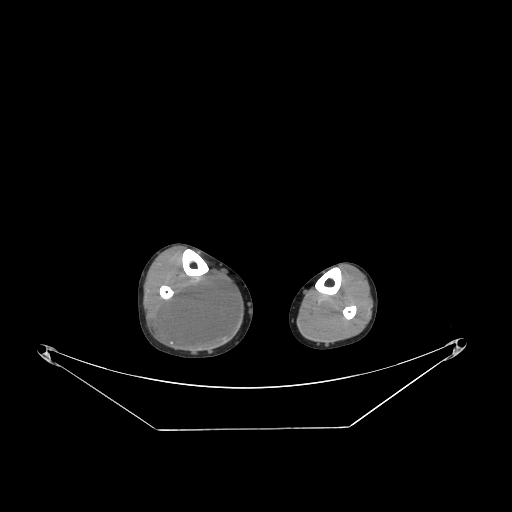
CT of an extremity soft-tissue mass (from a PET/CT study), one axial slice; slice 89 of 267 in the series (ordered by position); reconstruction kernel STANDARD; 140 kVp; soft-tissue window (W 400 / L 40 HU); 512 × 512 image matrix, field of view 500 × 500 mm. Male patient. Case-level facts recorded for this patient, not image findings: histological type: liposarcoma - round cell; grade: high; site of the primary tumour: right calf.
Annotated regions visible in this slice (expert contour drawn on MRI and transferred to this co-registered scan by the dataset authors):
- gross tumour volume (mass): bounding box <155,274,238,348> (left, top, right, bottom; pixels)